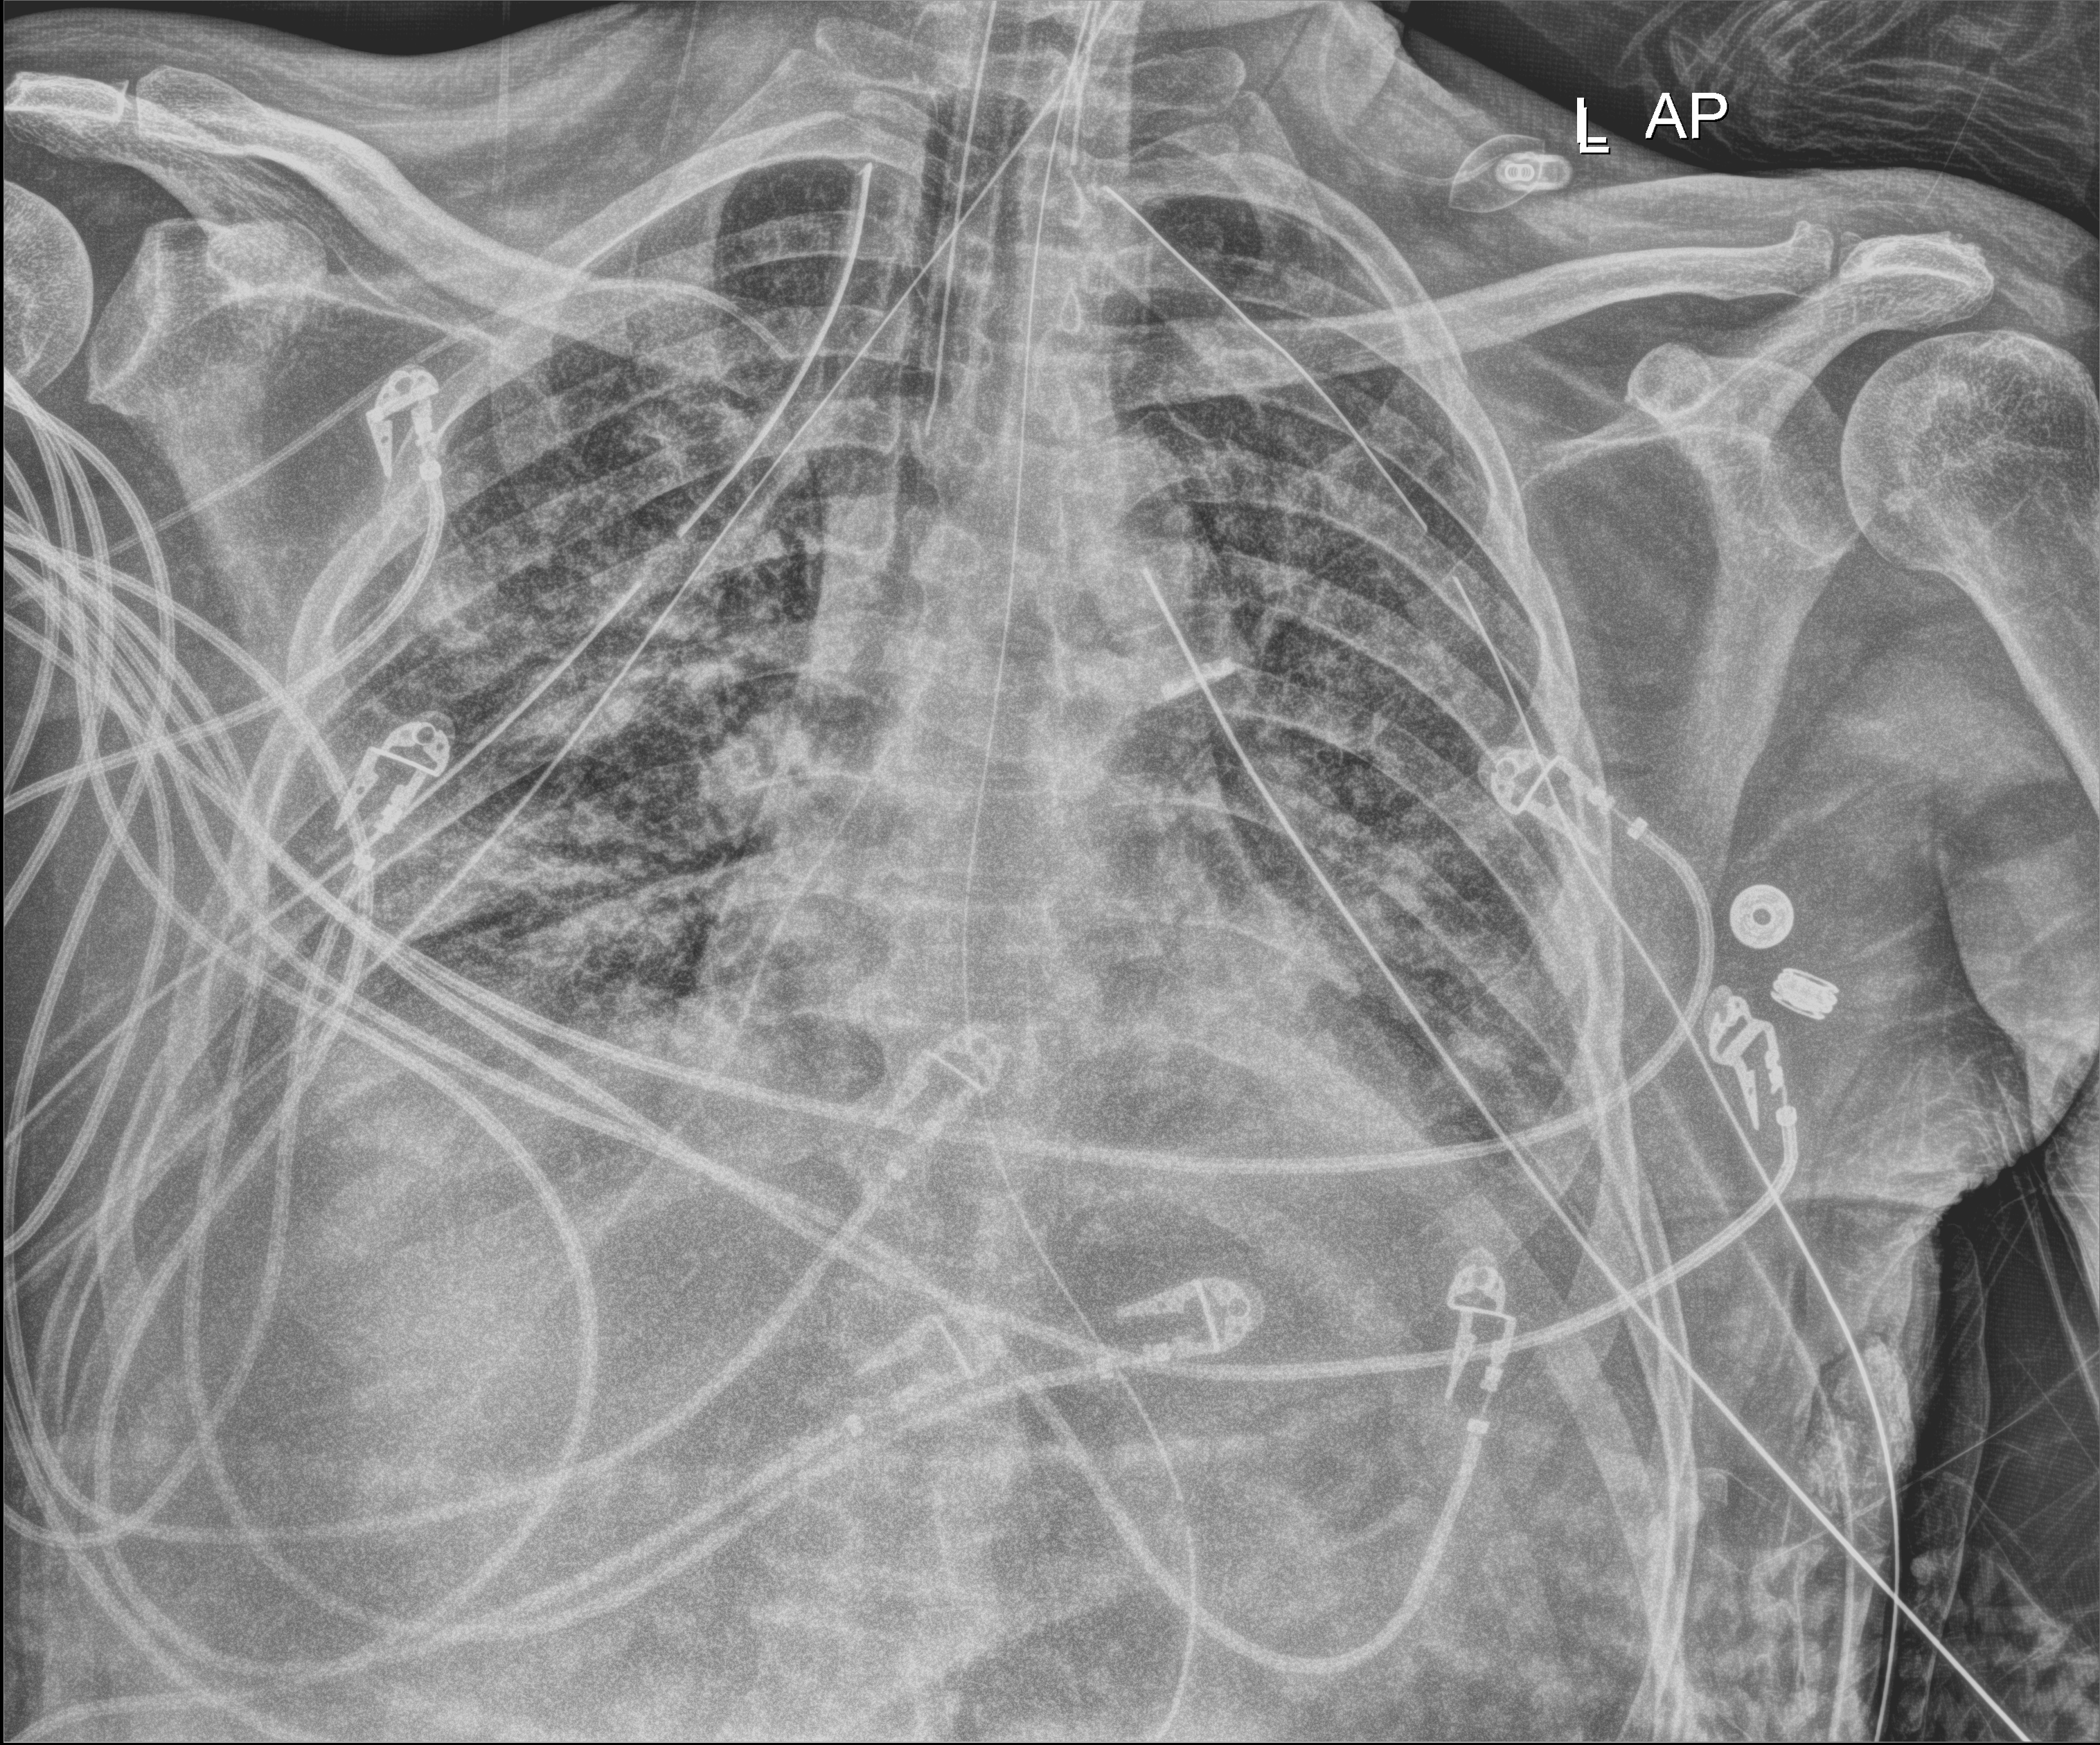
Portable chest radiograph, anteroposterior (AP) projection. Male patient hospitalised with COVID-19, age 18–59 years.
Hospital-stay facts (about this admission, not read from this image; timing relative to this image not recorded): mechanically ventilated during this hospital stay: yes; chronic kidney disease (admission record): no; COPD (admission record): no.